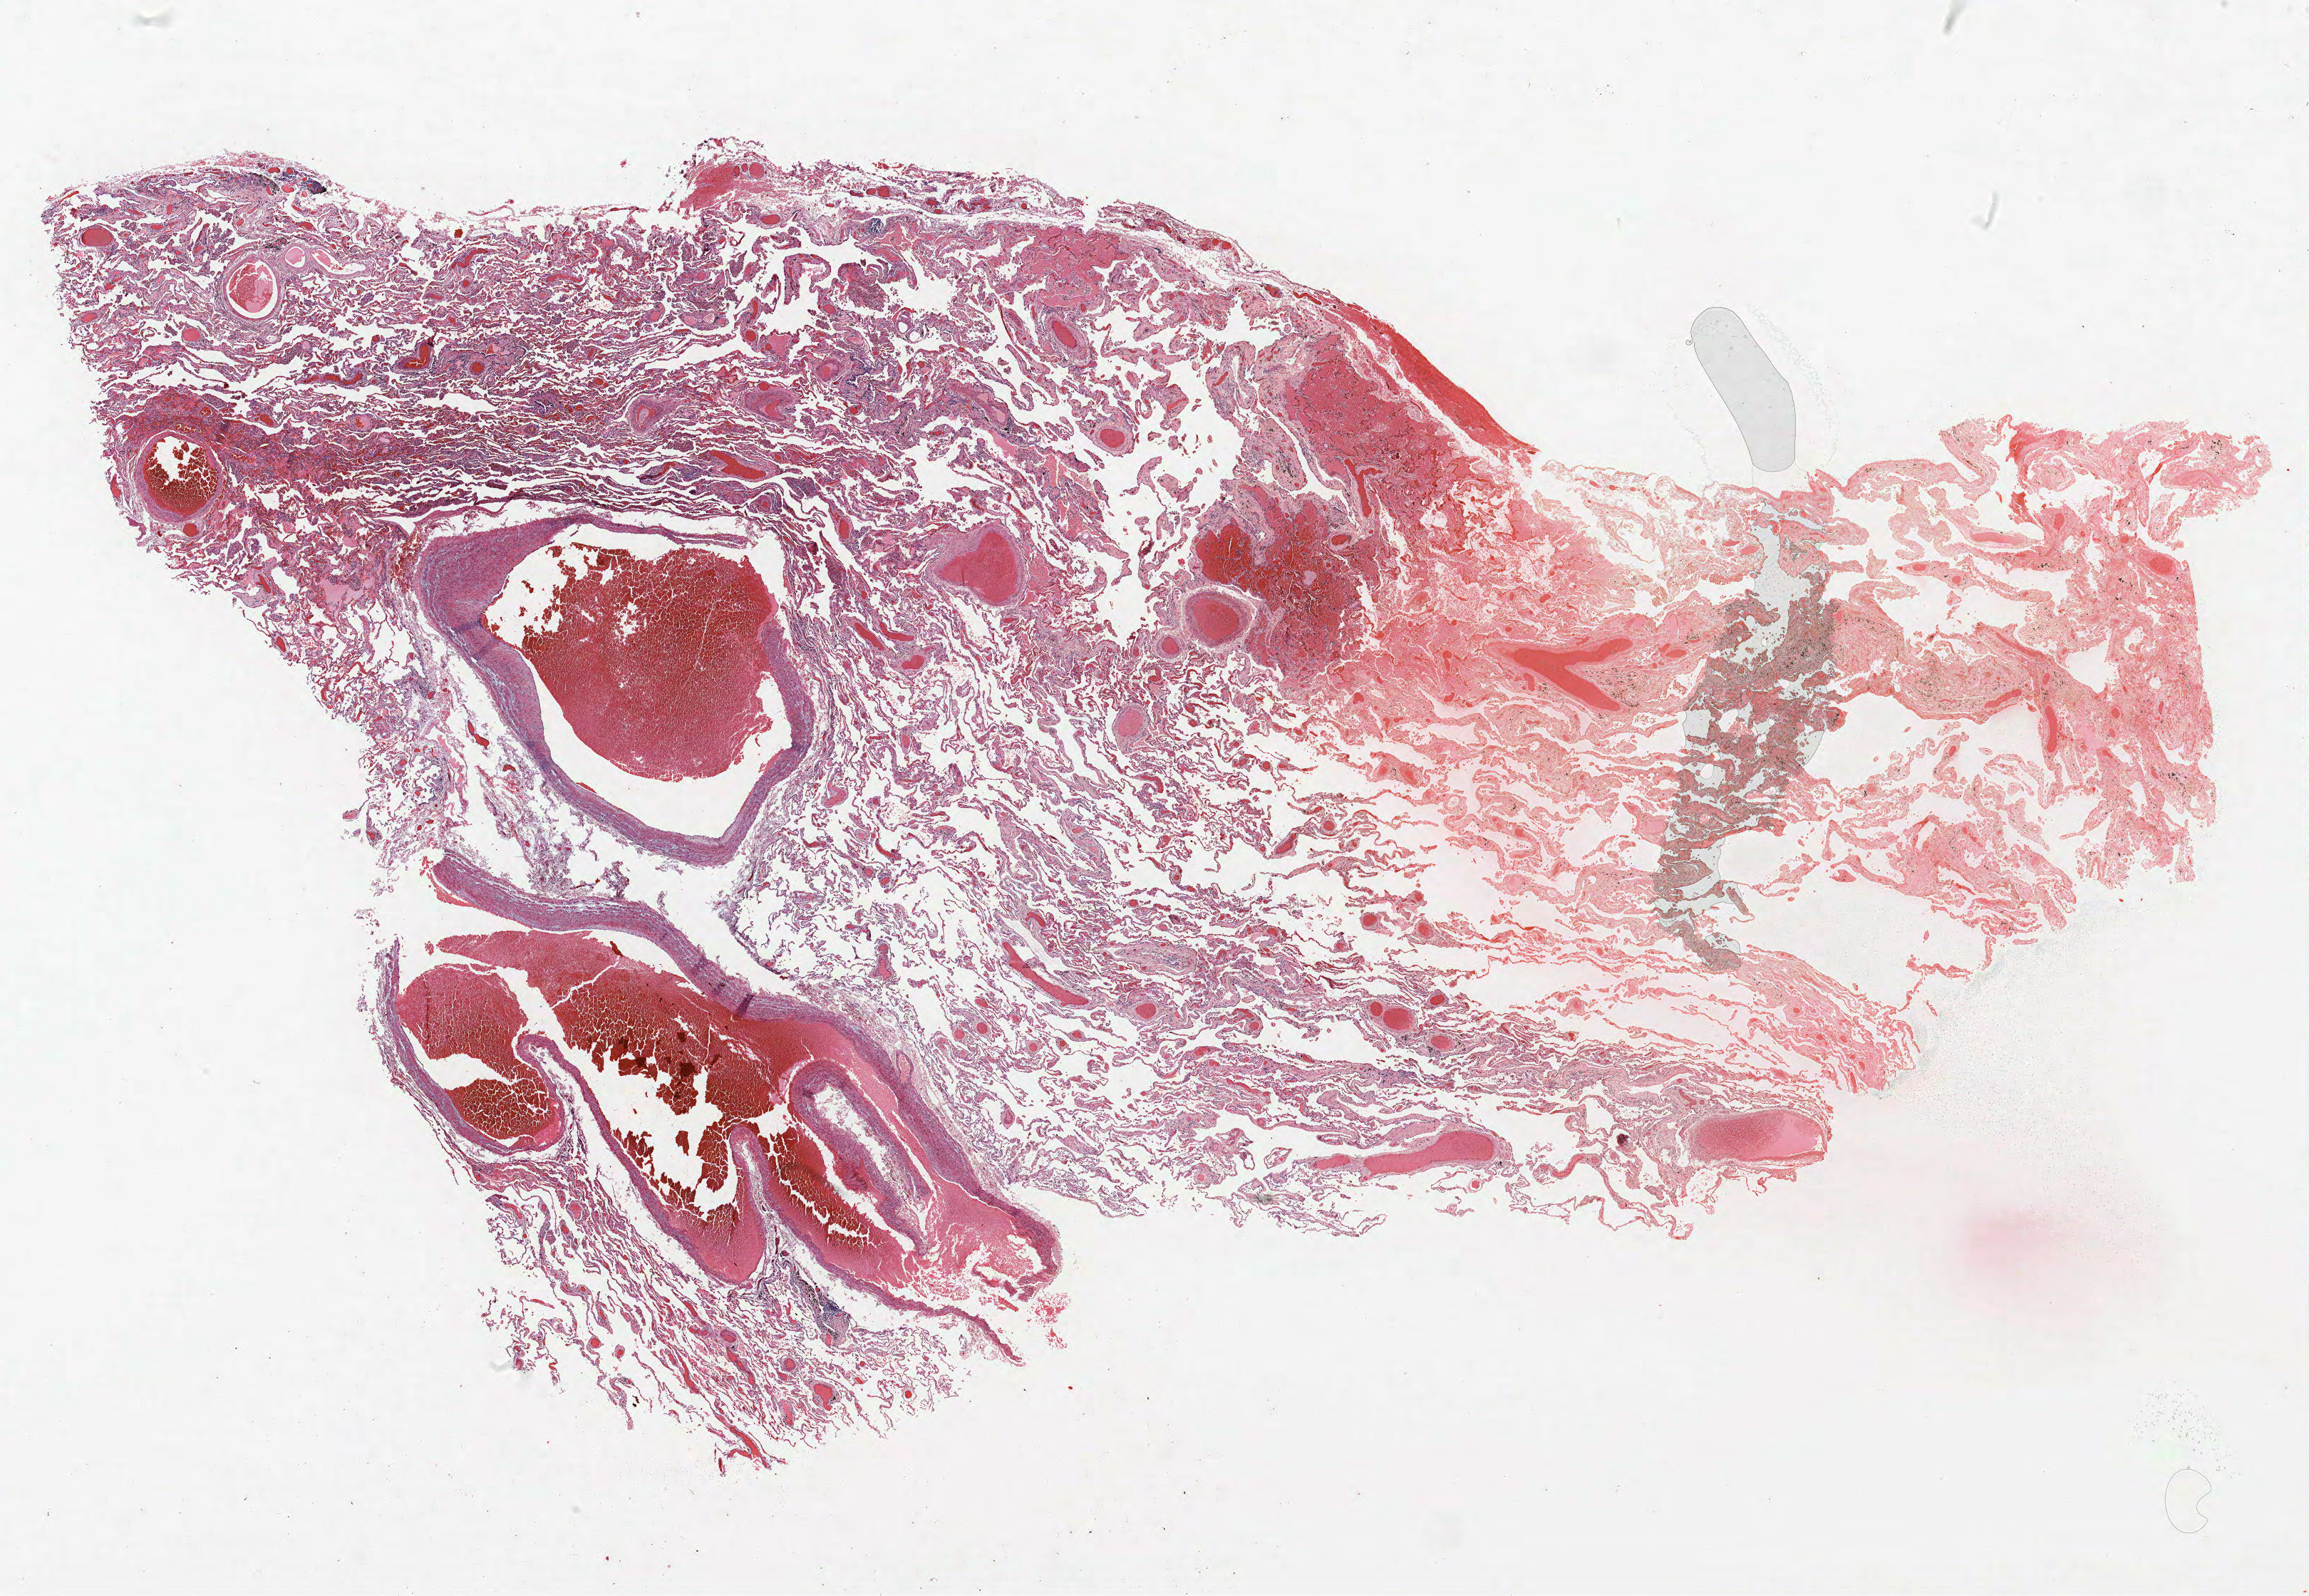
Whole-slide histology image, H&E-stained, shown as a low-resolution overview of the whole scanned area (about 25.9 x 17.9 mm). Formalin-fixed paraffin-embedded (FFPE) section. Lung. Male patient, aged 58 at enrolment. Current smoker at enrolment.
Participant's lung-cancer diagnosis: Large cell neuroendocrine carcinoma (ICD-O-3 8013/3).